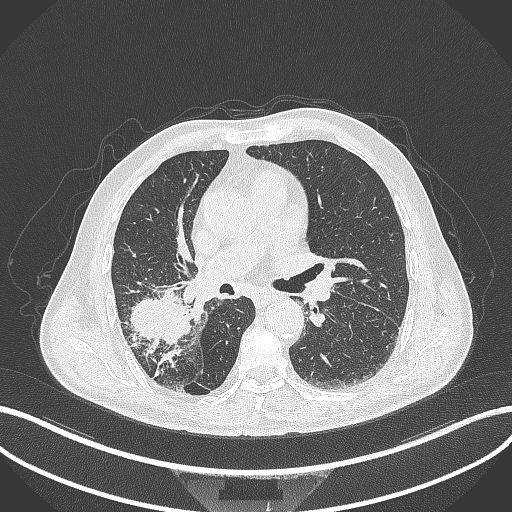
Chest CT, one axial slice. Position 232 of 429 along the scan axis. Lung window (W 1500 / L -600 HU). 512 × 512 image matrix. Patient: male, 72 years. Case-level facts recorded for this patient, not image findings: clinical TNM (as recorded): T3 N2 M0.
Outlined on this slice (bounding box drawn by a radiologist):
- lung tumour (recorded histology: adenocarcinoma): bounding box [x1, y1, x2, y2] px = [125, 292, 195, 348]